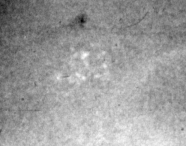
Region of interest cut from a scanned film mammogram (one marked finding); left breast; MLO view.
- Marked abnormality: calcifications, morphology punctate, distribution clustered; BI-RADS assessment category 4; pathology (as recorded): malignant.